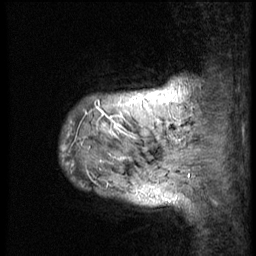
Breast MRI (dynamic contrast-enhanced), one sagittal slice; position 5 of 58 along the scan axis; 3 images stored at this slice position (order not interpretable as contrast timing); 1.5 T; TE 4.2 ms, TR 9 ms; 2.5 mm slice thickness; 256 × 256 image matrix, field of view 180 × 180 mm. Female patient, age 50 years. From the clinical record (not read from this slice): setting: breast cancer imaged before/during neoadjuvant chemotherapy; receptor status: triple-negative.
Structures marked on this image (semi-automatically segmented with operator editing):
- analysis volume of interest (the breast-tissue region the enhancement analysis was run in; not a lesion): bounding box (x1, y1, x2, y2) in pixels: (61, 62, 186, 214)
- tumour enhancement mask (voxels above the 140 % enhancement threshold inside the analysis volume of interest): (69, 99, 142, 159)